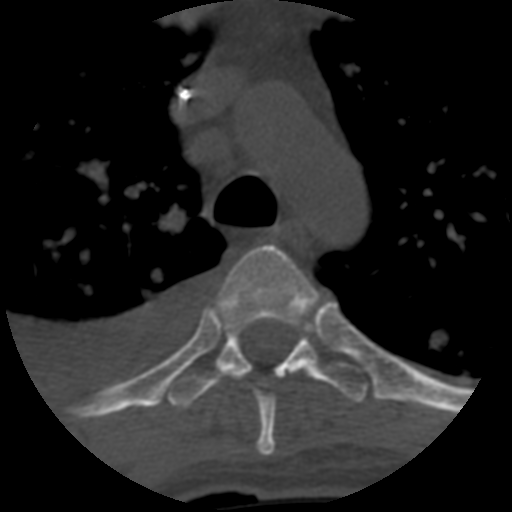
CT including the spine, one axial slice; position 462 of 708 along the scan axis; 120 kVp; one of 3 acquisitions stored at this slice position; bone window (W 1800 / L 400 HU); 1.25 mm slice thickness; 512 × 512 image matrix, field of view 160 × 160 mm. Patient age 55 years. From the clinical record (not read from this slice): primary cancer: colon; vertebrae with lytic lesions (as recorded): T12, L1, L5.
Outlined on this slice (semi-automatically segmented with operator editing):
- T4 vertebra: bounding box (x1, y1, x2, y2) in pixels: (216, 243, 315, 456)
- T5 vertebra: (167, 318, 368, 409)